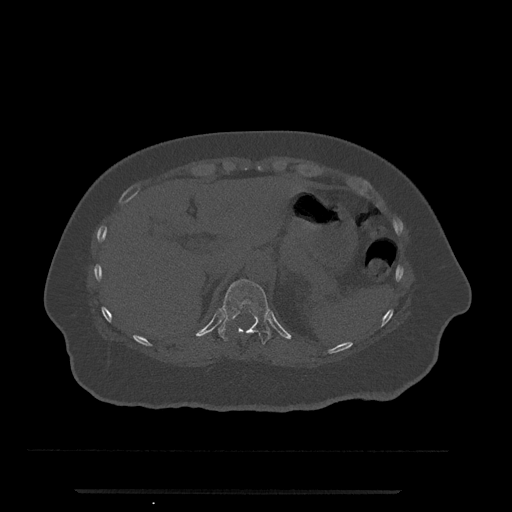
CT including the spine, one axial slice. Position 236 of 797 along the scan axis. Reconstruction kernel Br40s/3. 120 kVp. Bone window (W 1800 / L 400 HU). 512 × 512 image matrix, field of view 440 × 440 mm. Patient: female, 51 years. Case-level facts recorded for this patient, not image findings: primary cancer: neuro; vertebrae with lytic lesions (as recorded): T8.
Annotated regions visible in this slice (semi-automatically segmented with operator editing):
- T11 vertebra: box from (x=218, y=279) to (x=271, y=345) px